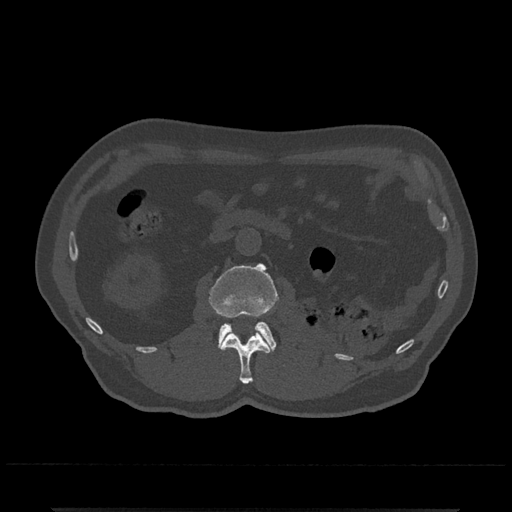
CT including the spine, one axial slice. Slice 323 of 797 in the series (ordered by position). 120 kVp. Bone window (W 1800 / L 400 HU). 0.5 mm slice thickness. 512 × 512 image matrix. Male patient, age 67 years. From the clinical record (not read from this slice): primary cancer: prostate.
Outlined on this slice (semi-automatically segmented with operator editing):
- L1 vertebra: box from (x=220, y=330) to (x=270, y=384) px
- L2 vertebra: (x=210, y=263)–(x=278, y=352)